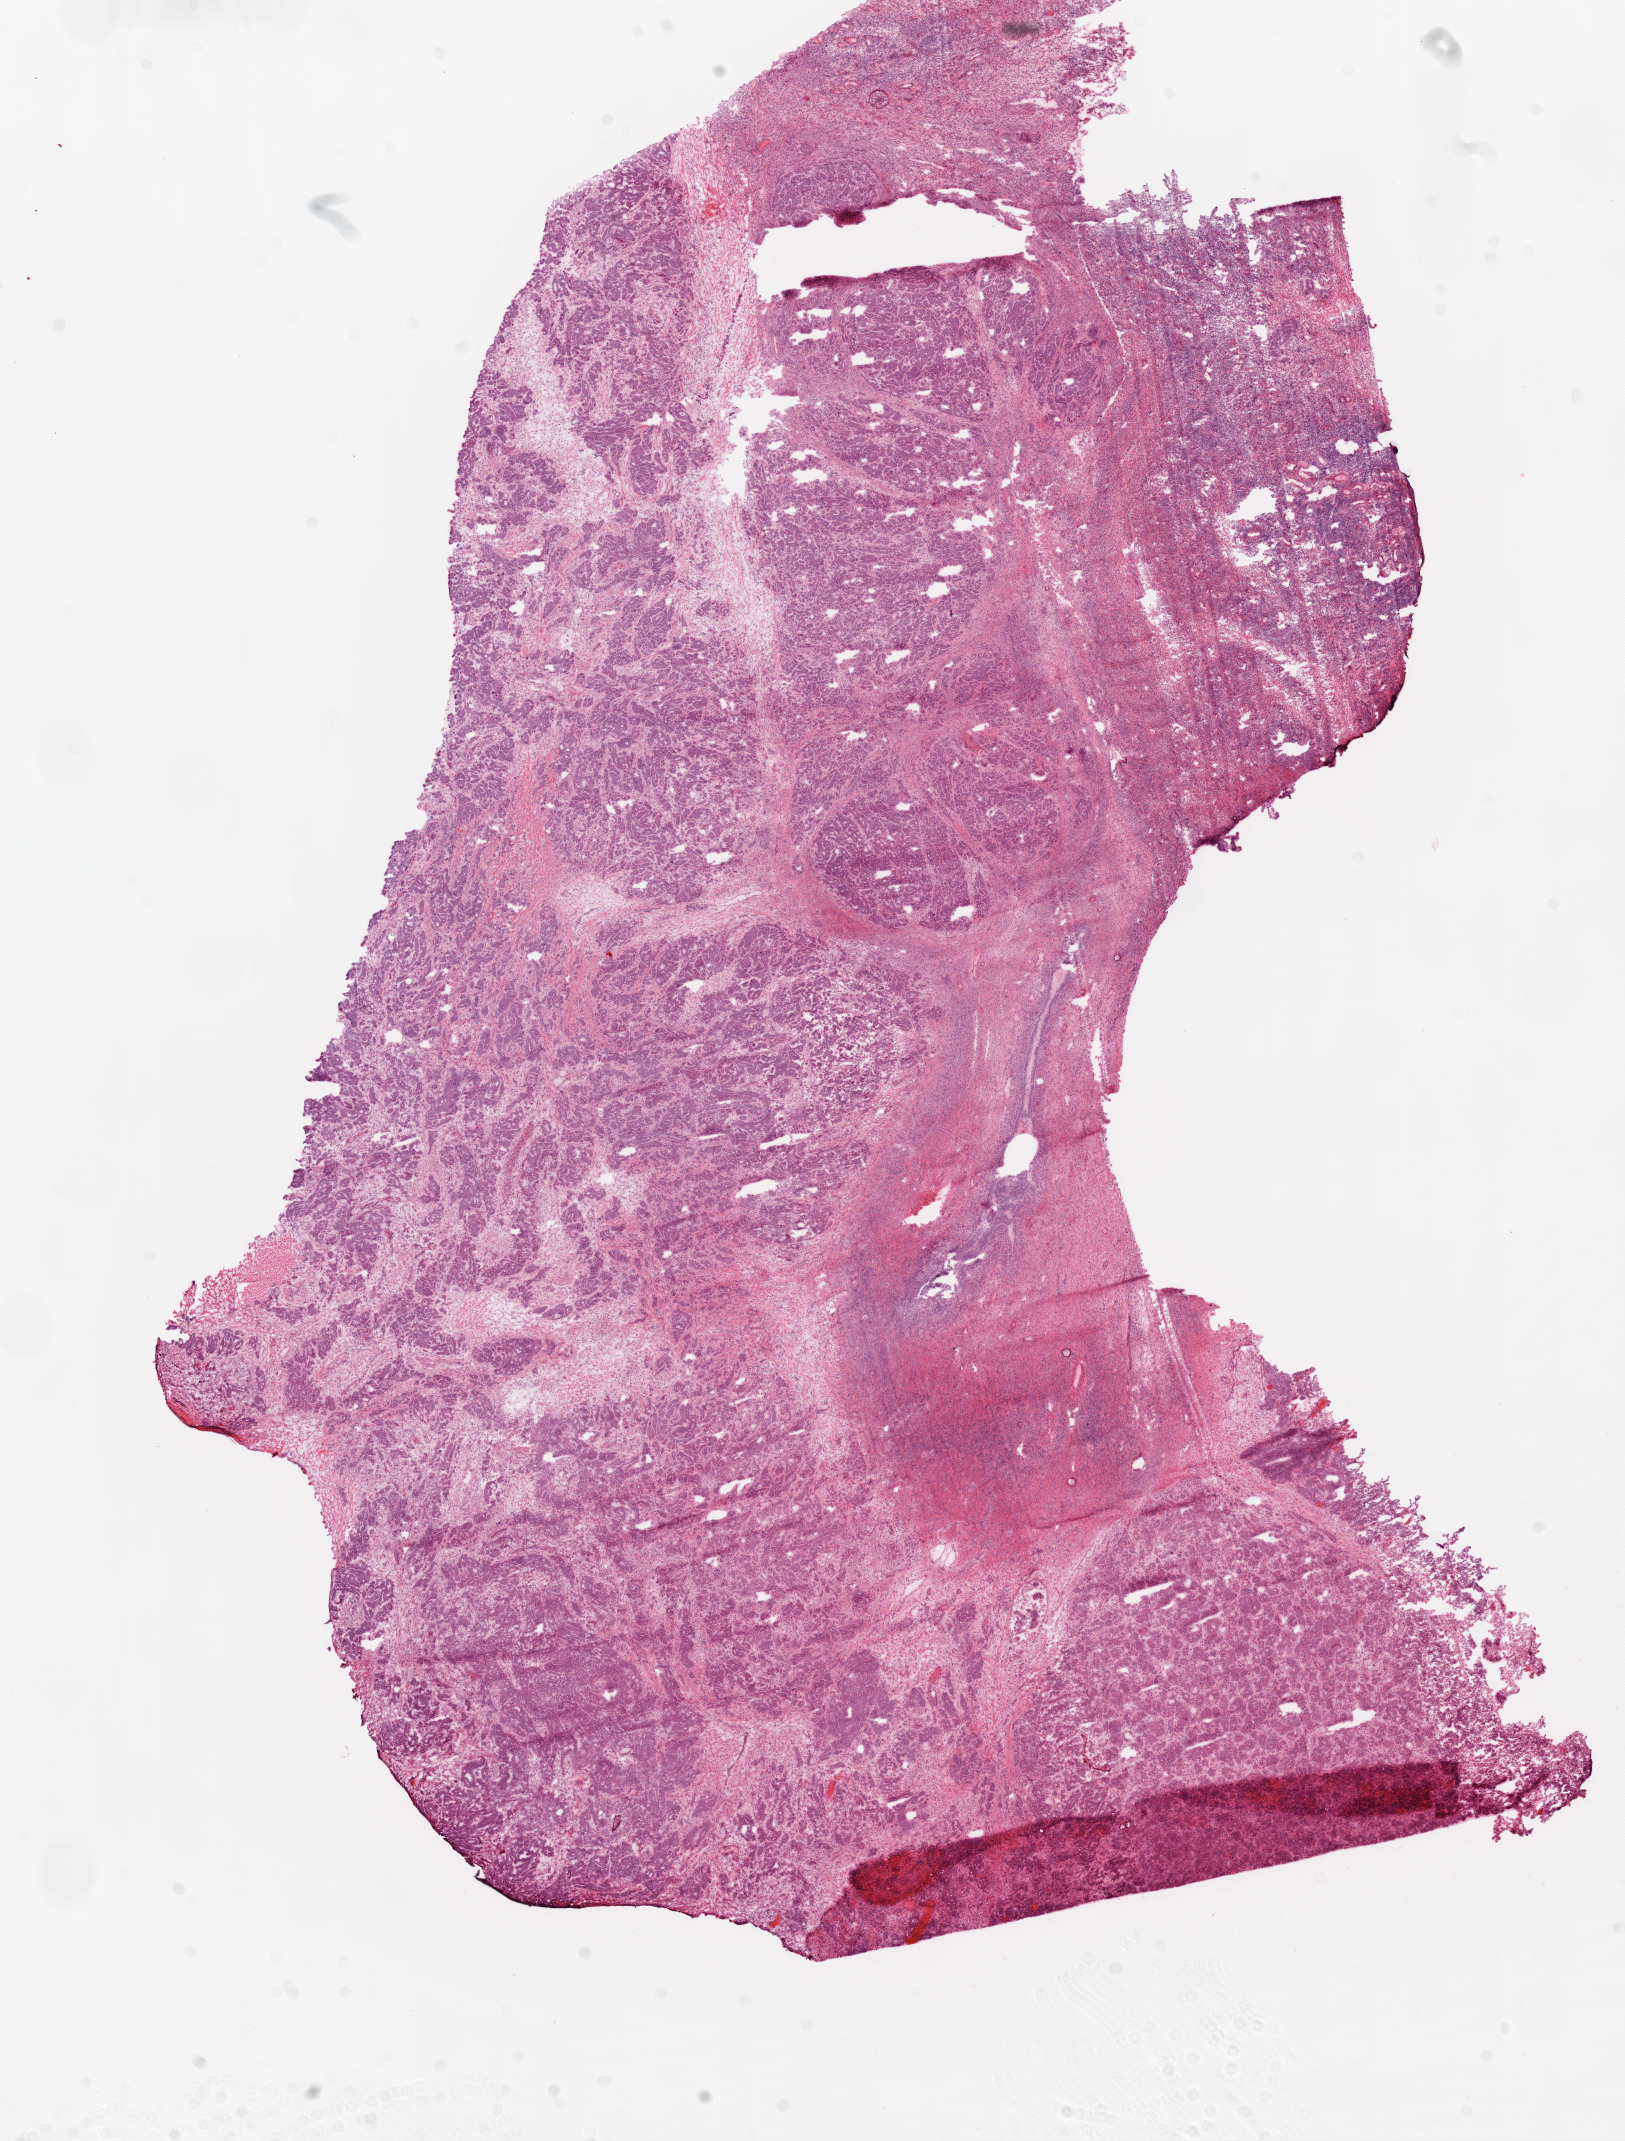
Digitized Hematoxylin and eosin (H&E) stained tissue section (whole slide) — a low-resolution overview of the entire scanned area, about 13.0 x 17.2 mm, frozen section from the top of the tissue portion, sample: primary tumour, ovary. Female patient; age at initial diagnosis 38 years. Histologic grade: G3 (poorly differentiated). Pathologist review of this section (percent, as recorded): tumour cells 70%, tumour nuclei 70%, normal cells 1%, stromal cells 28%, necrosis 1%.
Laterality: bilateral. Pathologic diagnosis: Serous cystadenocarcinoma, NOS. FIGO stage: IIIC.